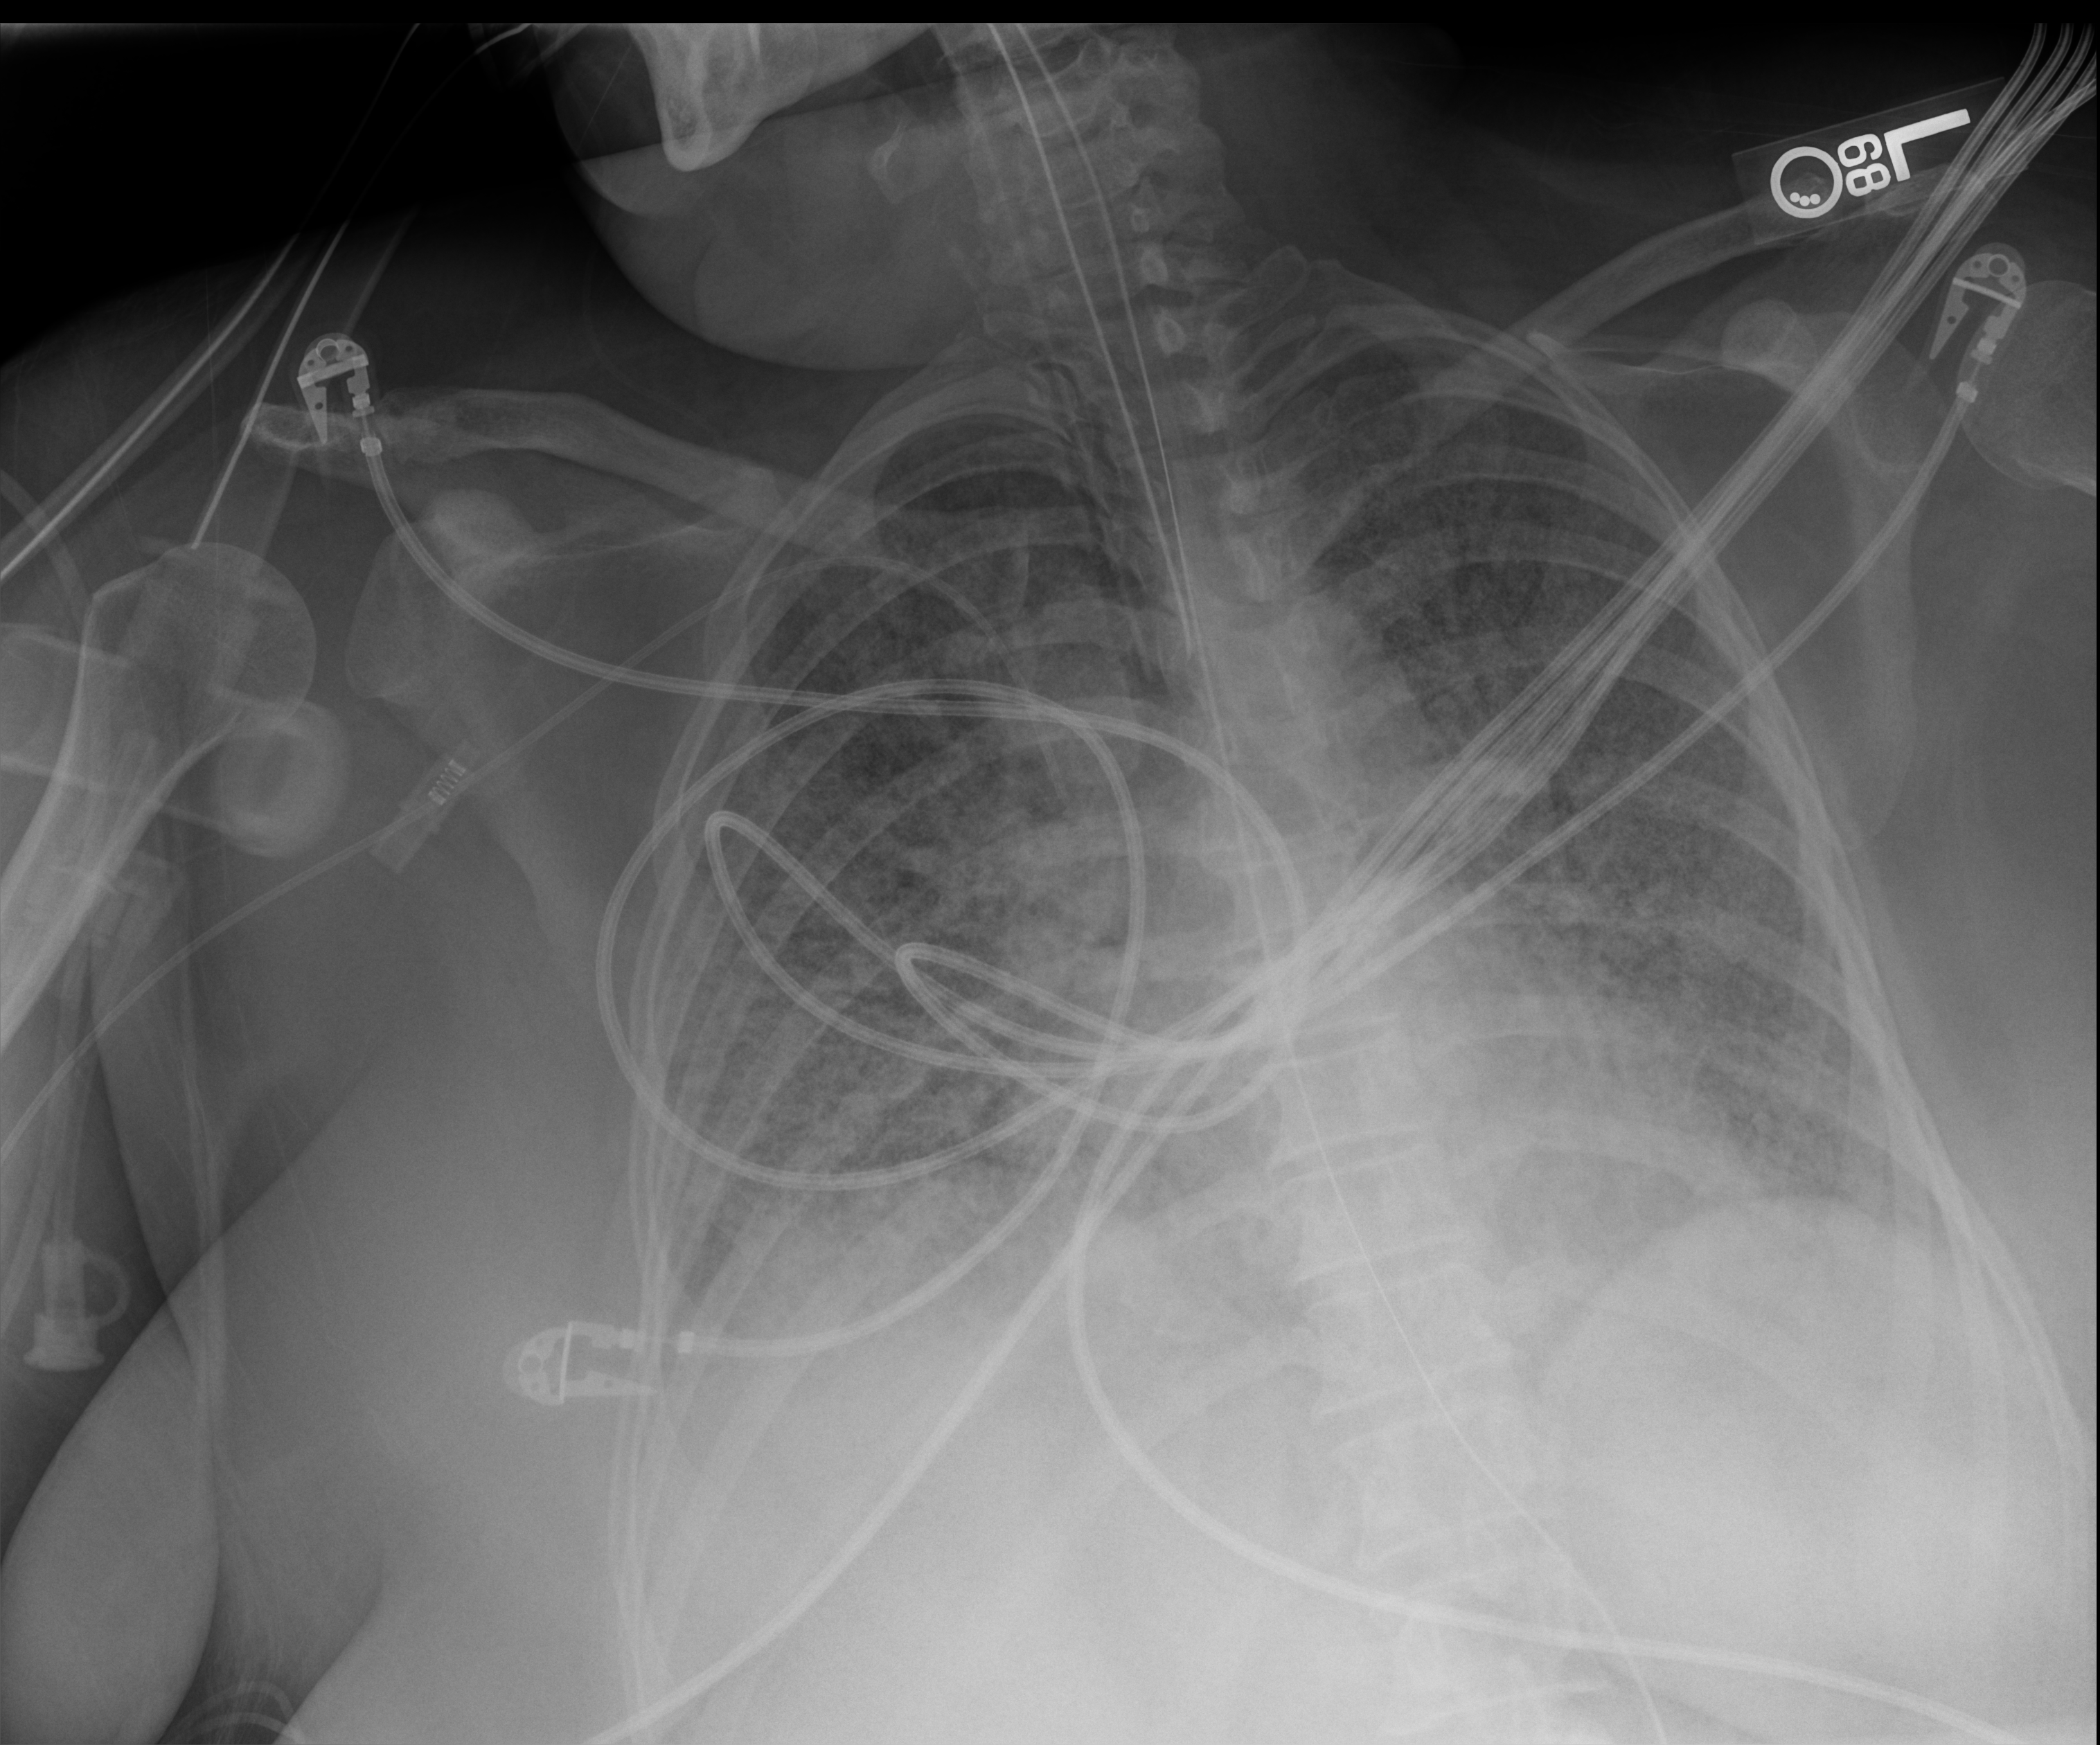
Chest X-ray (portable), anteroposterior (AP) projection. Patient hospitalised with COVID-19; female, aged 18–59 years.
Hospital-stay facts (about this admission, not read from this image; timing relative to this image not recorded):
- length of hospital stay: 95 days
- mechanically ventilated during this hospital stay: yes